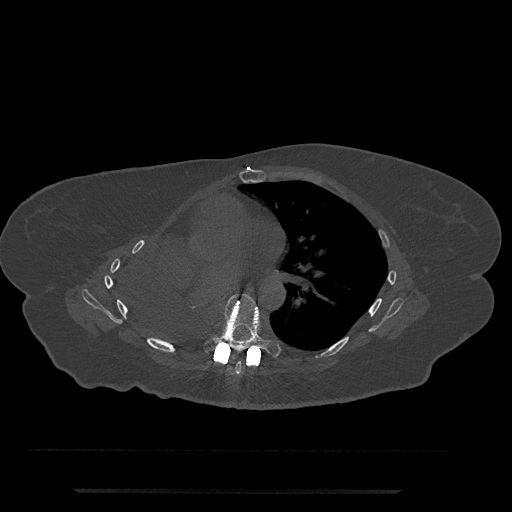
CT including the spine, one axial slice; slice 450 of 797 in the series (ordered by position); reconstruction kernel Br40s/3; bone window (W 1800 / L 400 HU); 0.5 mm slice thickness; 512 × 512 image matrix, field of view 440 × 440 mm. Patient: female, 51 years. From the clinical record (not read from this slice): primary cancer: neuro; vertebrae with lytic lesions (as recorded): T8.
Structures marked on this image (semi-automatic segmentation, software-assisted and operator-edited):
- T6 vertebra: bounding box <220,361,242,375> (left, top, right, bottom; pixels)
- T7 vertebra: <204,294,281,356>